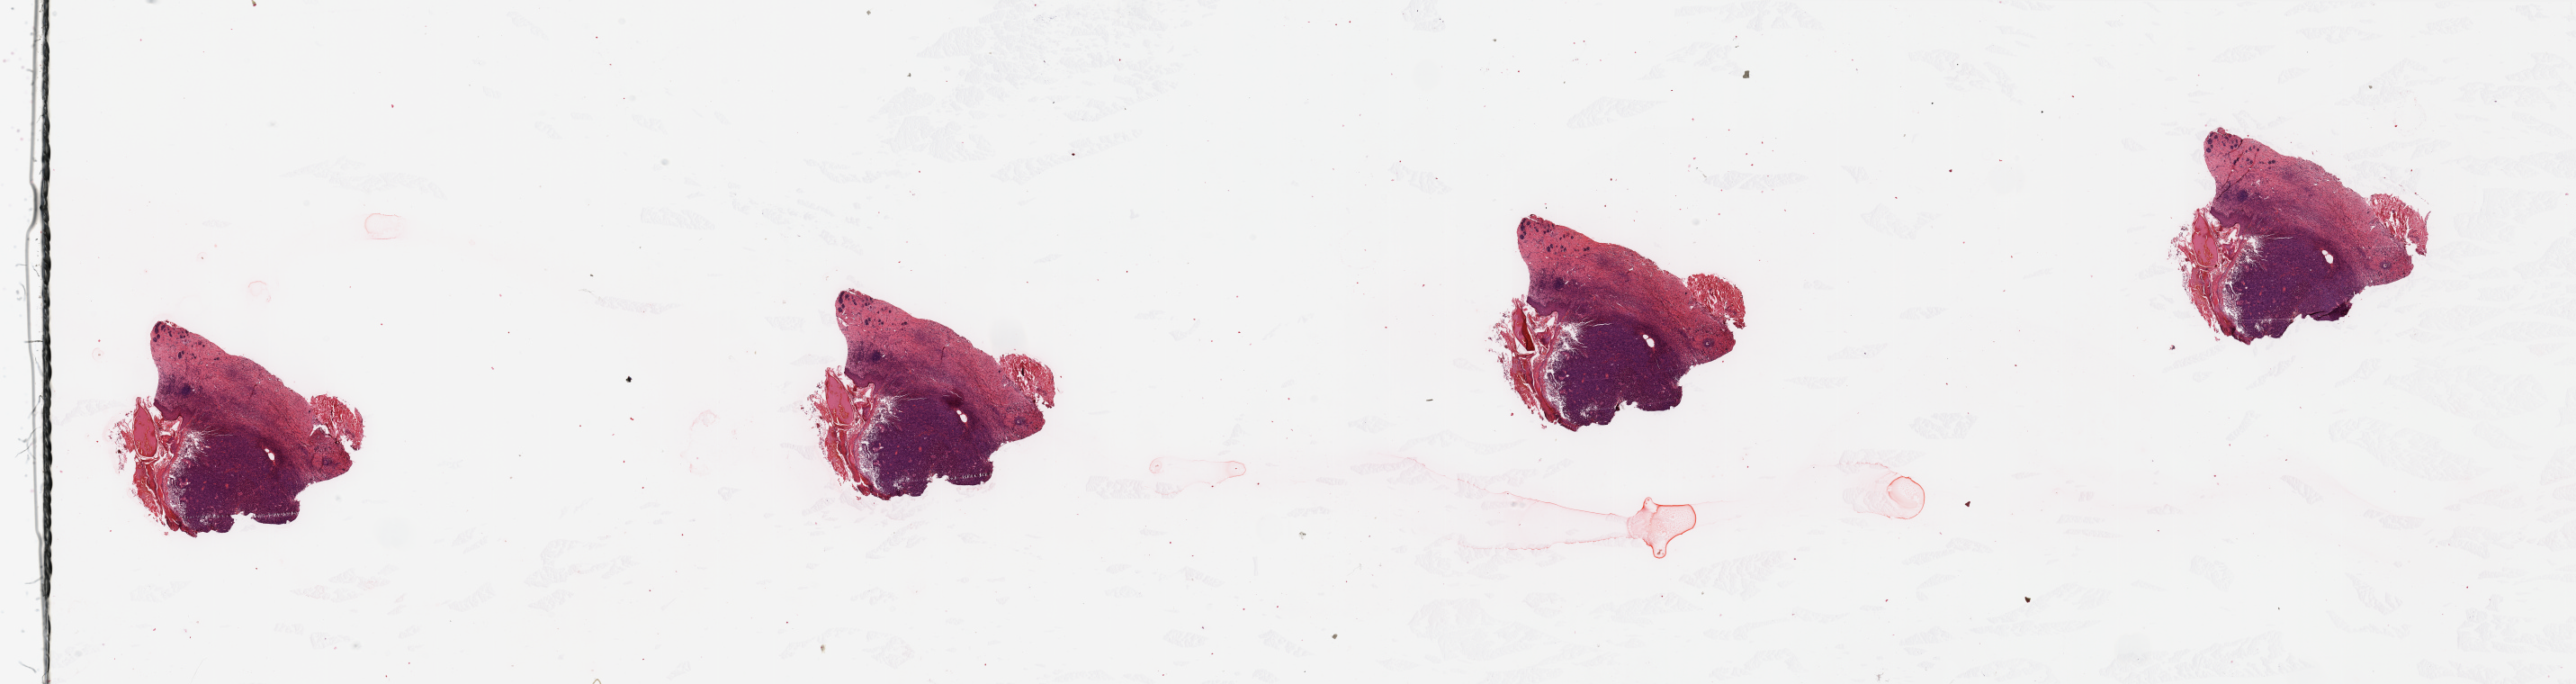
Whole-slide histology image, H&E-stained — a low-resolution overview of the entire scanned area, about 45.3 x 12.0 mm; tumour tissue sample, sampled site: trunk. Male, 69 y/o. Slide review estimates, as recorded: tumour nuclei 90%, necrosis 0%.
Diagnosis: Malignant melanoma, NOS. Primary tumour site (as recorded): trunk. AJCC pathologic stage: IIA.